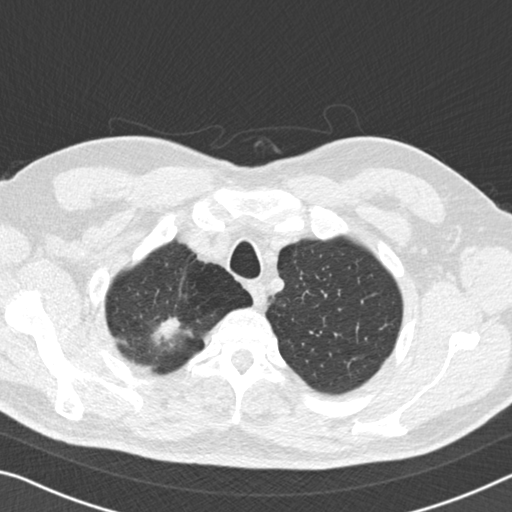
Chest CT (low-dose screening protocol), one axial image, third annual screen, lung window (W 1500 / L -600 HU), slice 23 of 167 in the series. Male, age 56 years at enrolment. Former smoker at enrolment.
Lesion marked by an expert reader, box from (x=140, y=306) to (x=202, y=359) px. Screening reader's record for this exam (one nodule recorded; not confirmed to be the boxed lesion): non-calcified nodule or mass ≥4 mm, right upper lobe, 13 × 13 mm, spiculated (stellate) margins, soft tissue attenuation, pre-existing on the prior screen: yes; interval growth: yes. Official screen result: positive, other. Later outcome: lung cancer diagnosed 97 days after this screen — adenocarcinoma, NOS, right upper lobe, moderately differentiated (G2), stage IA (AJCC 6th edition), 9 mm at pathology.